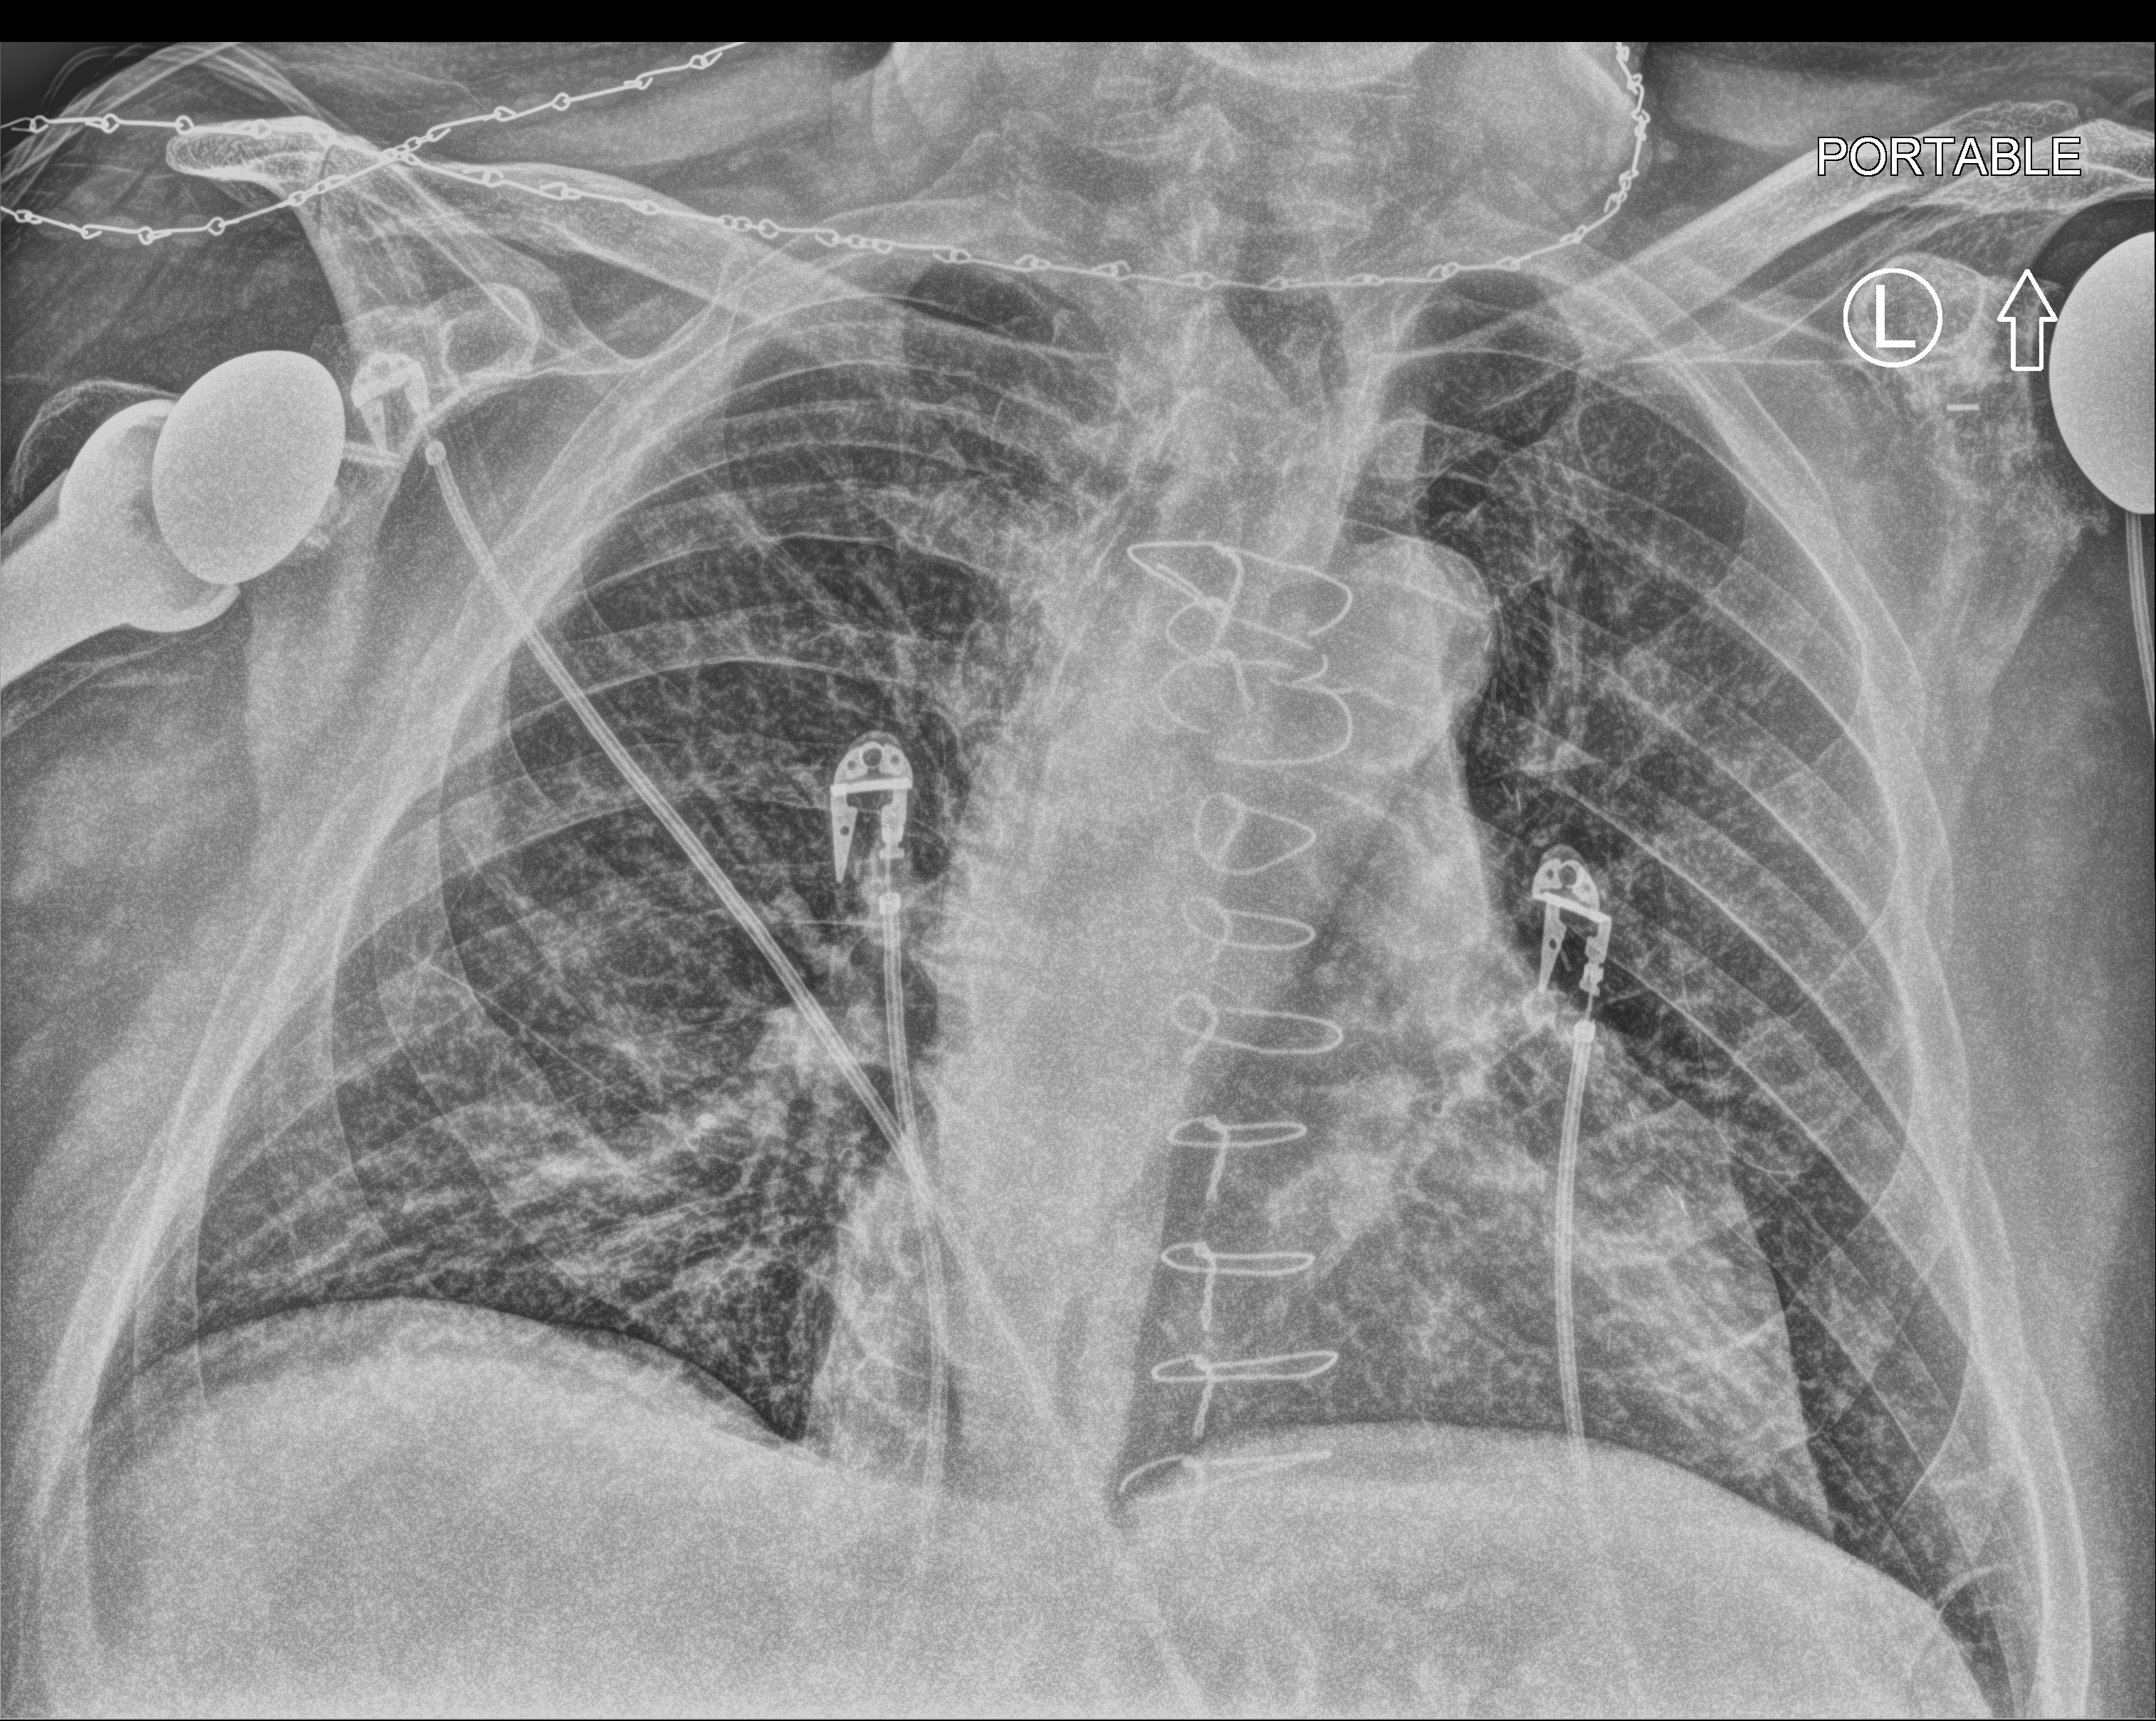
Bedside chest radiograph (computed radiography), anteroposterior (AP) projection. Patient hospitalised with COVID-19; male, aged 60–74 years.
From the hospital-stay record, not from the radiograph (when in the stay this image was taken is not recorded): admitted to intensive care during this hospital stay: no; mechanically ventilated during this hospital stay: no.